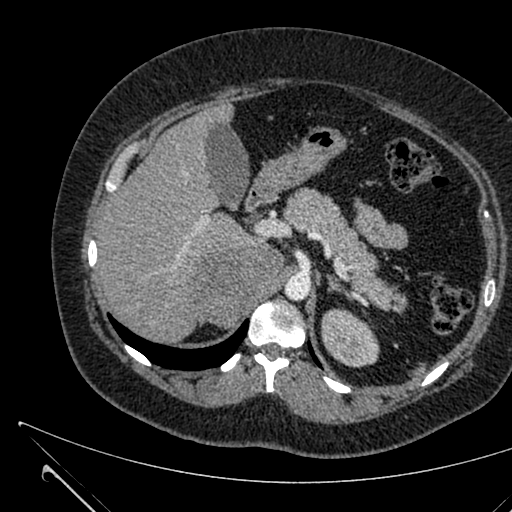
Contrast-enhanced abdominal CT, one axial slice; slice 445 of 731 in the series (ordered by position); intravenous contrast given; soft-tissue window (W 400 / L 40 HU); 1 mm slice thickness; 512 × 512 image matrix. Female patient, age 36 years. Case-level facts recorded for this patient, not image findings: diagnosis: adrenocortical carcinoma; tumour side: right adrenal; tumour size at pathology: 10 cm; Ki-67 index: 20 %; stage (as recorded): 4.
Annotated regions visible in this slice (semi-automatically segmented with operator editing):
- mass: bounding box (x1, y1, x2, y2) in pixels: (190, 247, 285, 327)